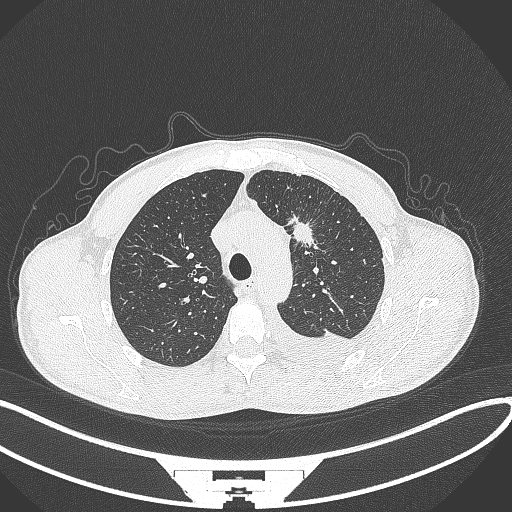
Chest CT, one axial slice. Position 248 of 371 along the scan axis. 120 kVp. Lung window (W 1500 / L -600 HU). 1 mm slice thickness. 512 × 512 image matrix, field of view 400 × 400 mm. Patient: male, 49 years. Case-level facts recorded for this patient, not image findings: clinical TNM (as recorded): T1c N1 M1.
Structures marked on this image (rectangle marked by the reading radiologist):
- lung tumour (recorded histology: adenocarcinoma): bounding box <289,214,315,250> (left, top, right, bottom; pixels)